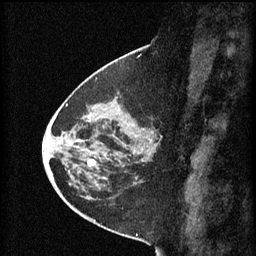
Breast MRI (dynamic contrast-enhanced), one sagittal slice. Position 30 of 60 along the scan axis. 3 images stored at this slice position (order not interpretable as contrast timing). 1.5 T. TE 4.2 ms, TR 8.2 ms. 2 mm slice thickness. 256 × 256 image matrix, field of view 200 × 200 mm. Female patient, age 45 years.
Structures marked on this image (semi-automatically segmented with operator editing):
- analysis volume of interest (the breast-tissue region the enhancement analysis was run in; not a lesion): bounding box (x1, y1, x2, y2) in pixels: (80, 102, 157, 171)
- tumour enhancement mask (voxels above the 70 % enhancement threshold inside the analysis volume of interest): (88, 160, 143, 167)